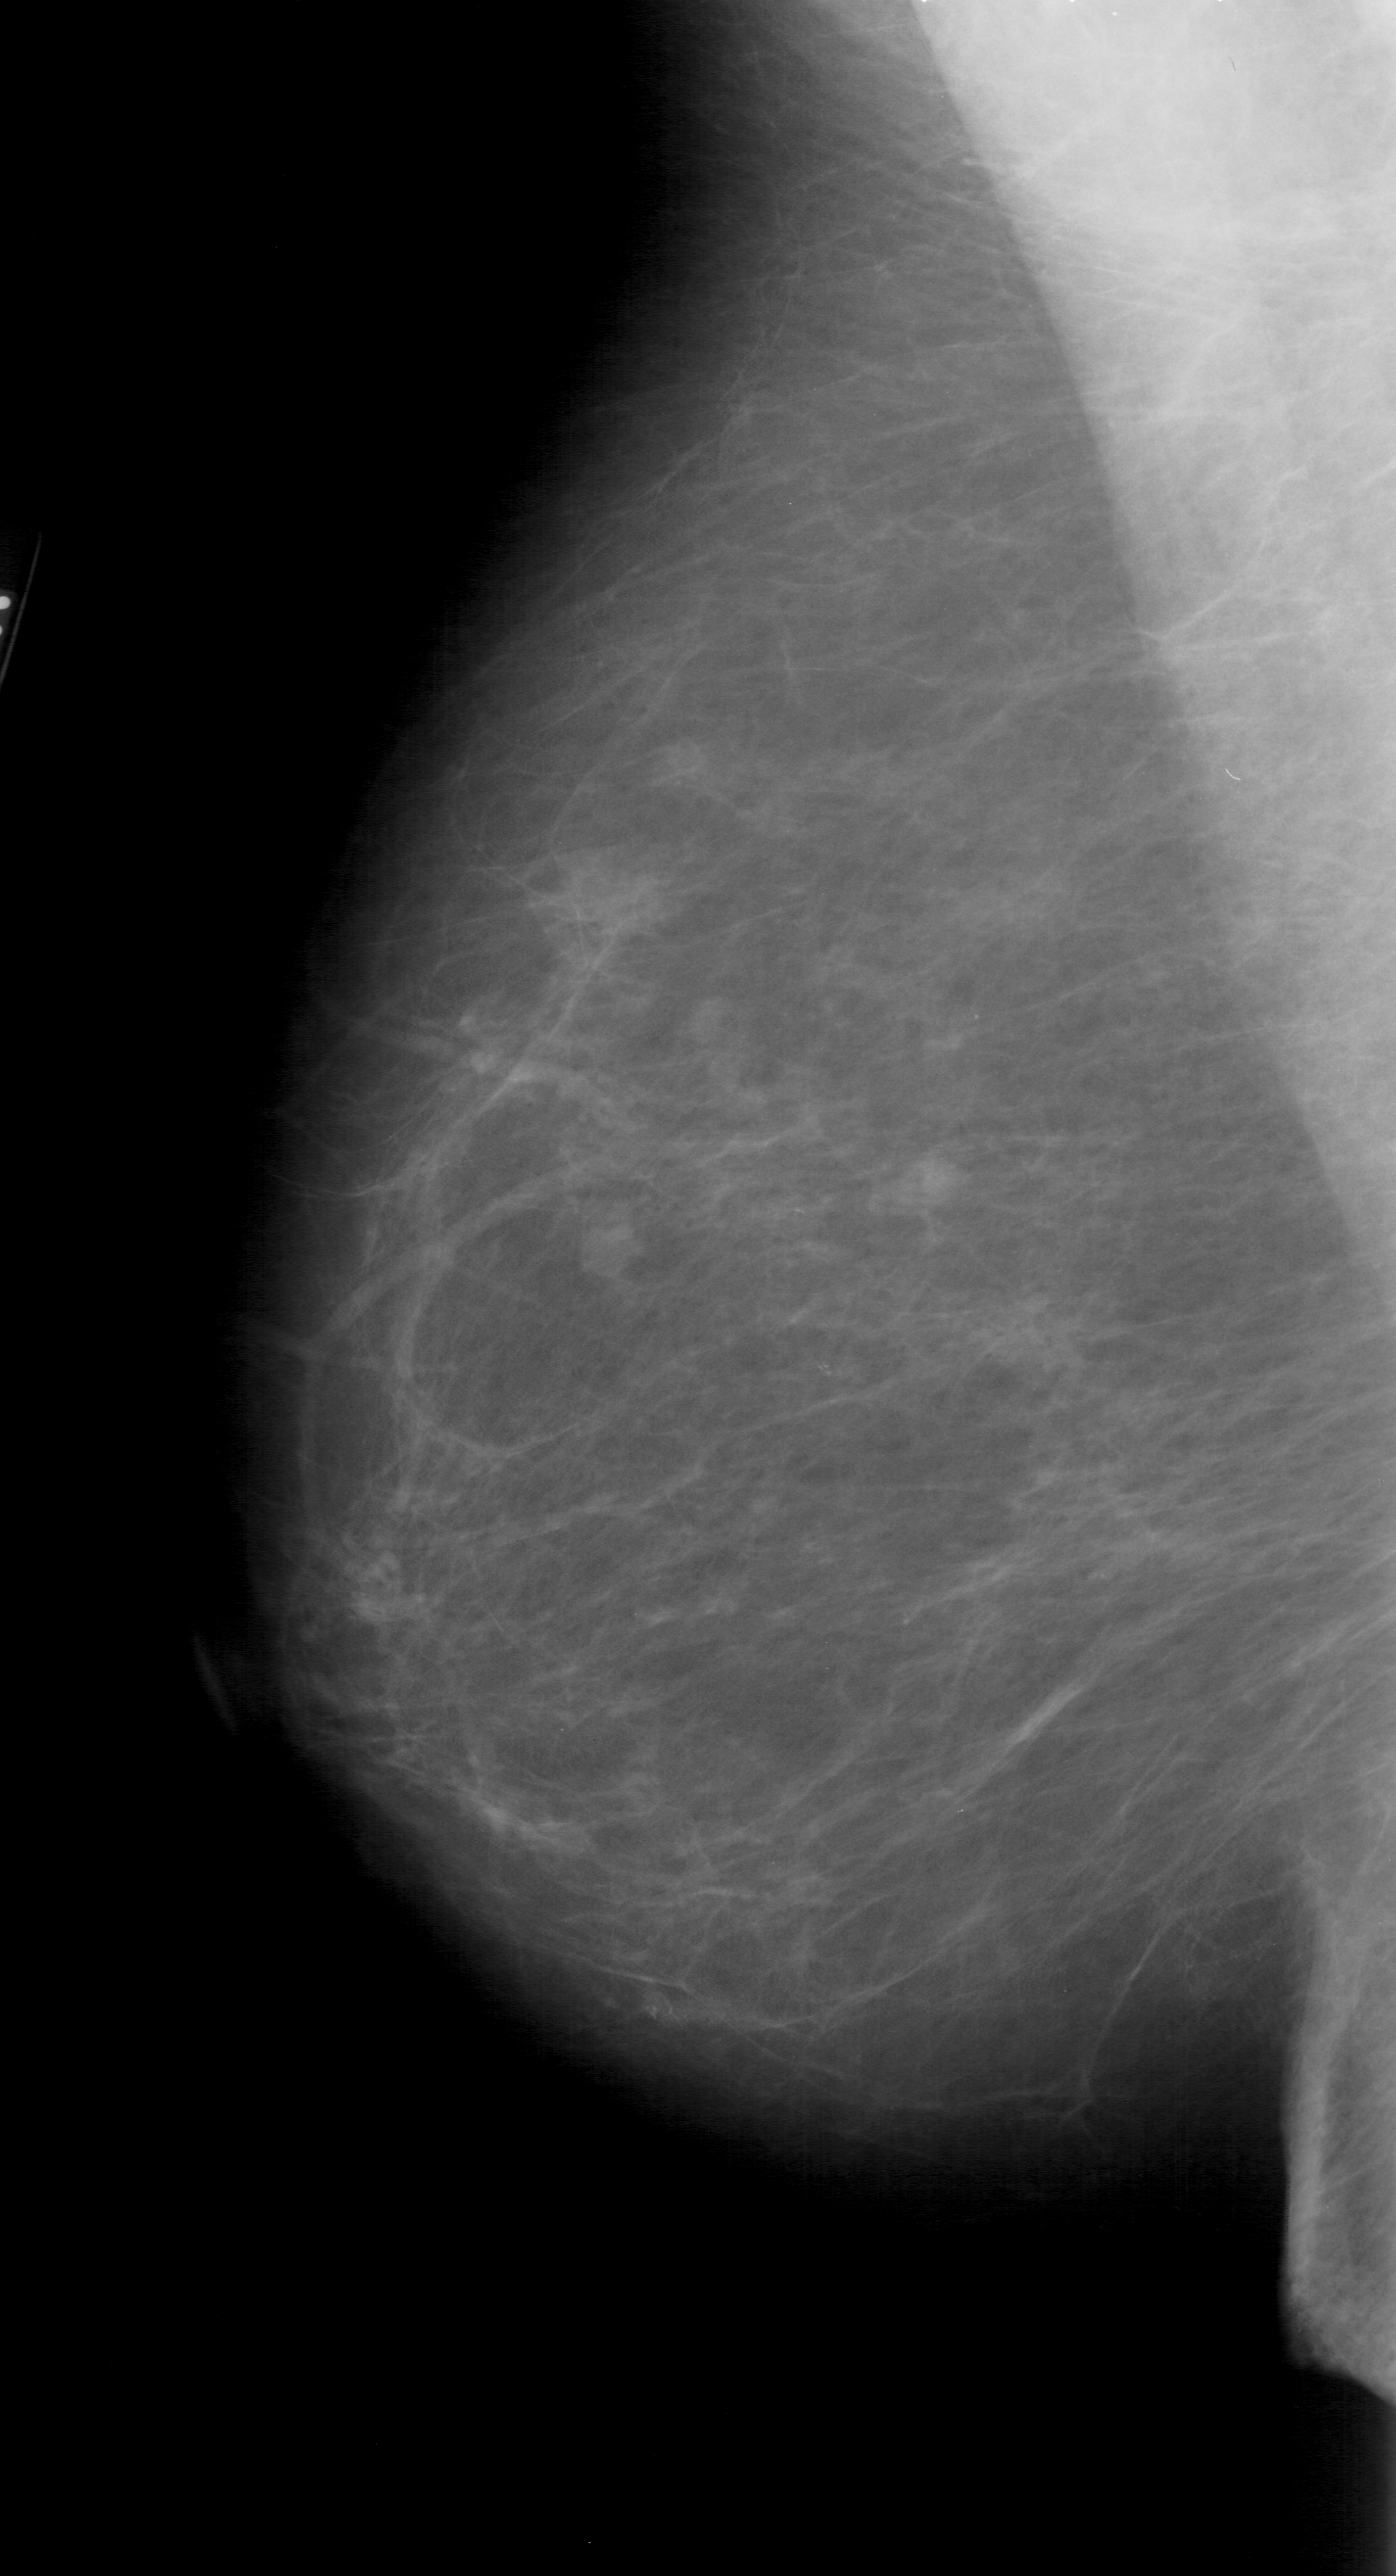
Digitized screen-film mammogram; left breast; MLO view; BI-RADS breast density category 2 (scale 1–4); 1396 × 2576 image matrix.
Marked abnormalities (boxes around the expert regions of interest):
- mass, shape lobulated, margins microlobulated; BI-RADS assessment category 4; subtlety rating 3 on a 1 (subtle) to 5 (obvious) scale; pathology result (as recorded, not read from the image): benign: bounding box (x1, y1, x2, y2) in pixels: (577, 1190, 652, 1292)